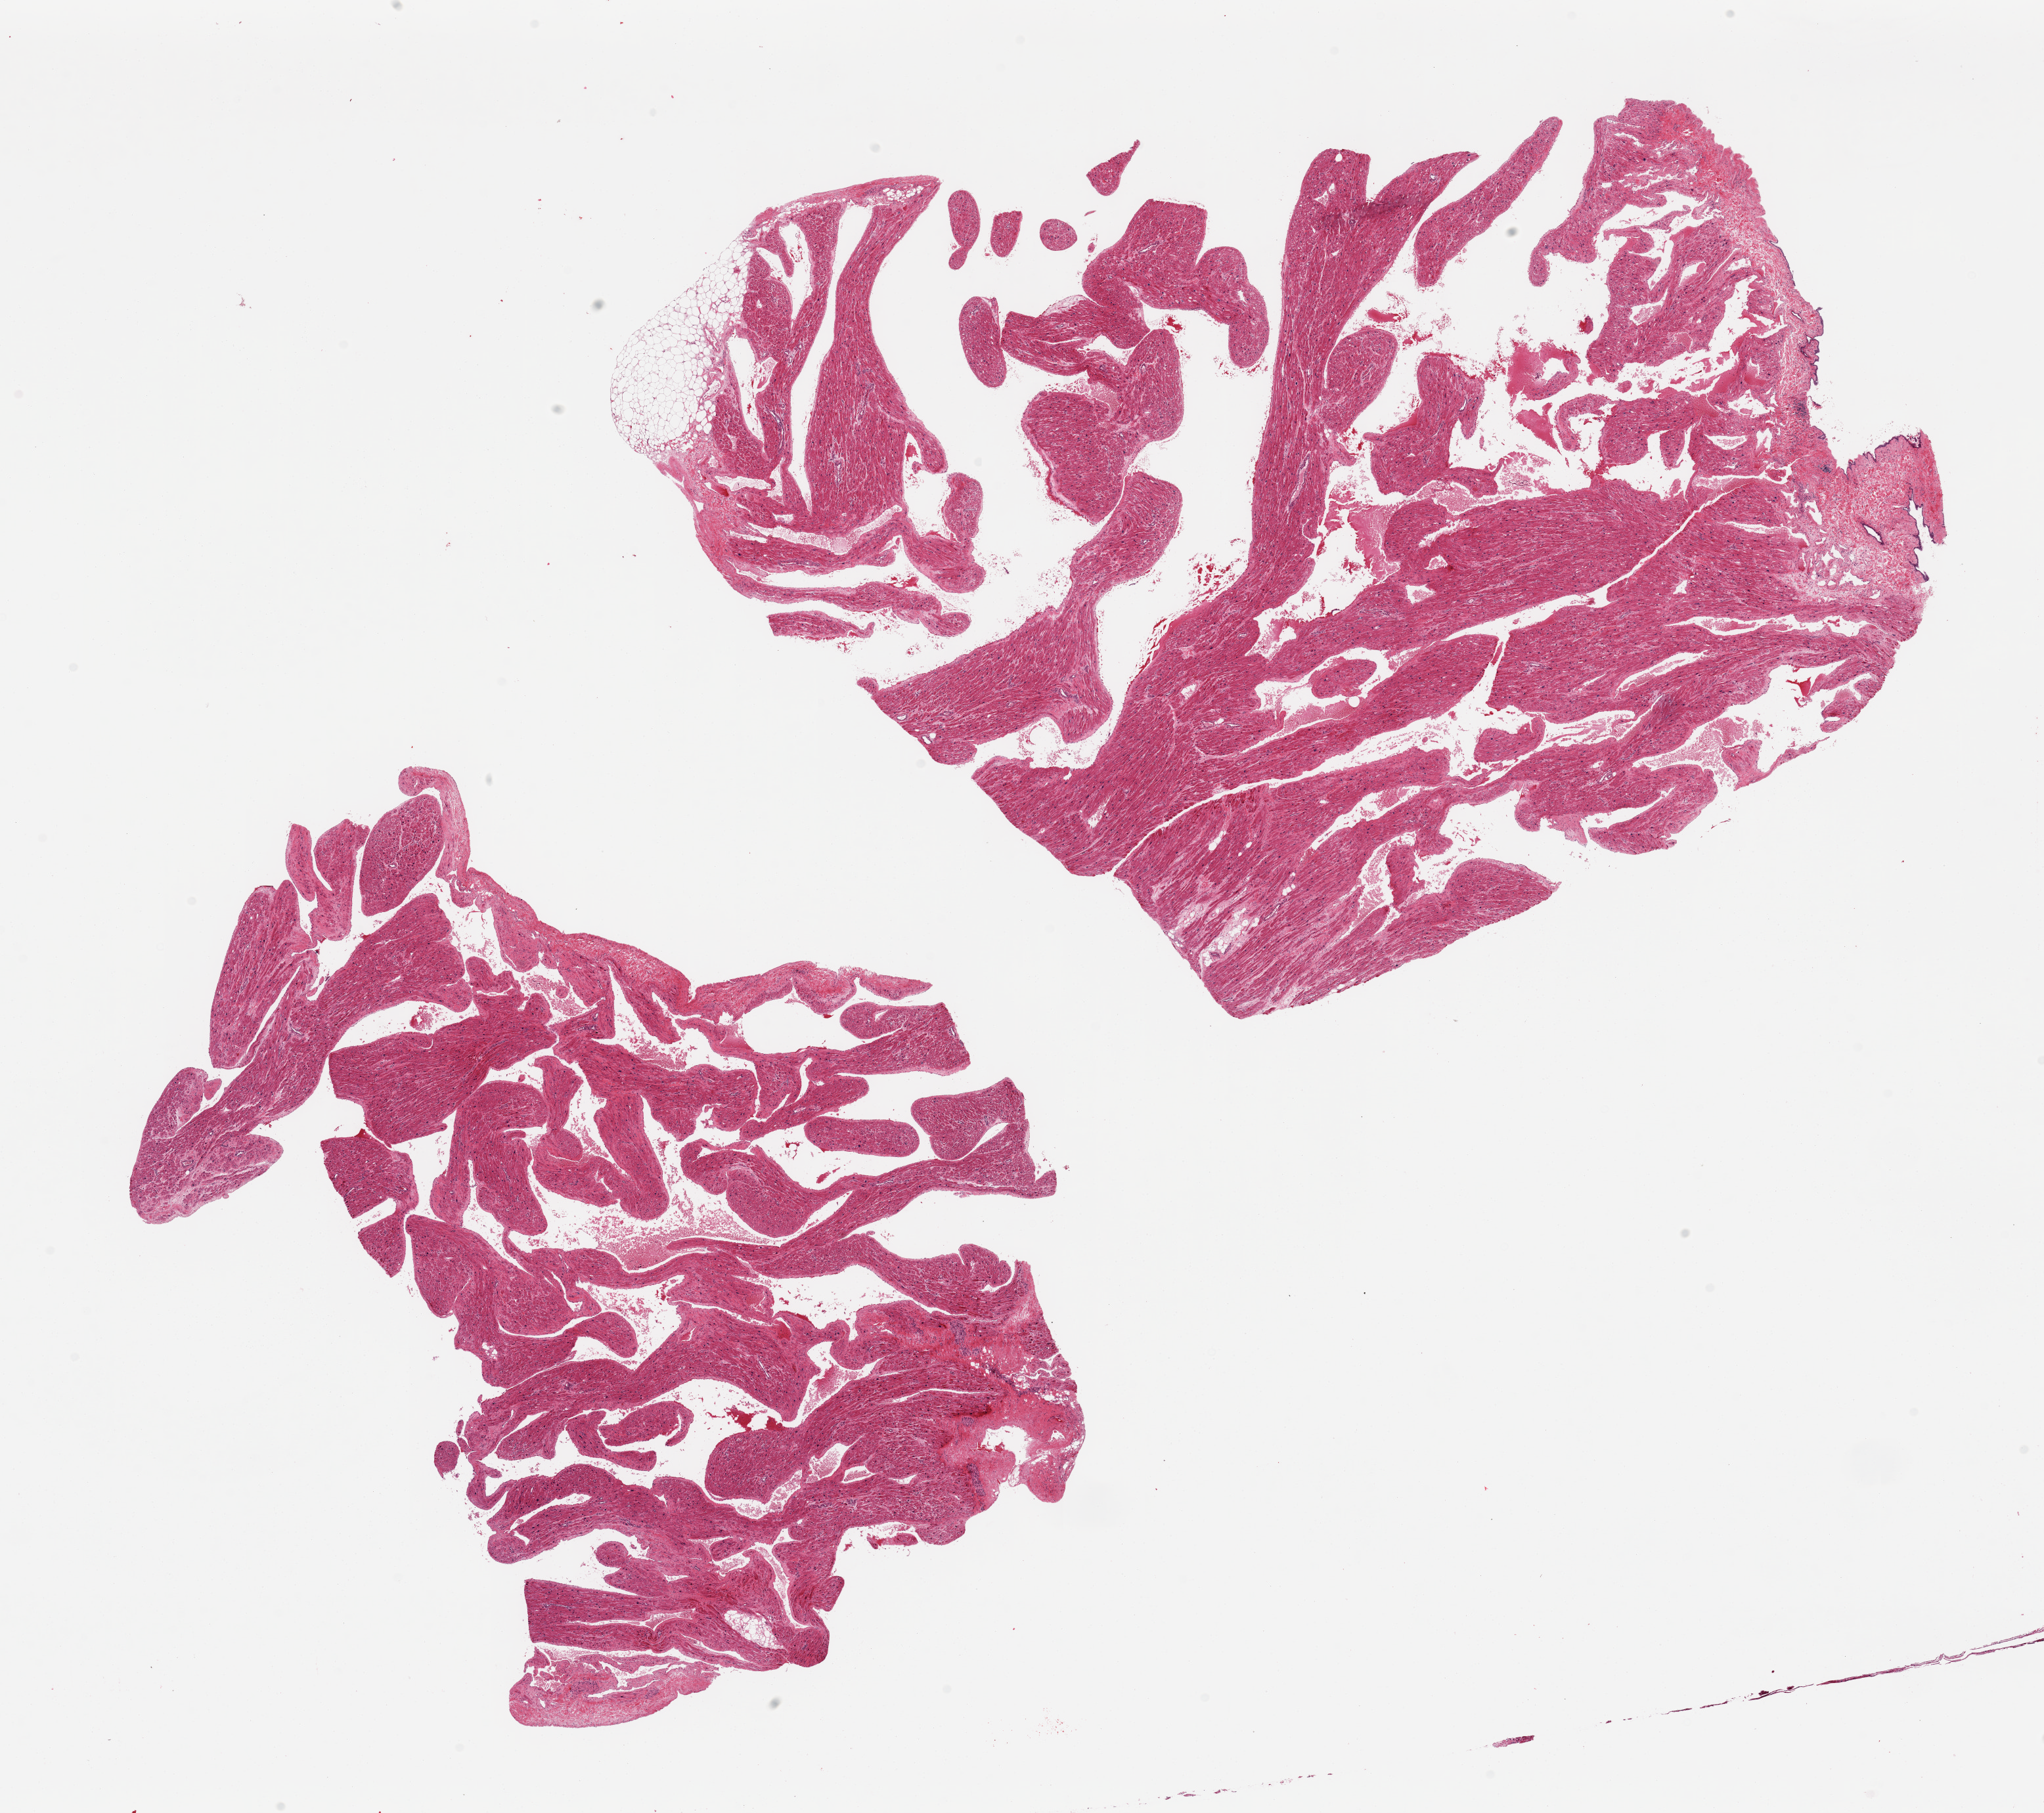
Whole-slide image, hematoxylin and eosin (H&E) stain — a low-resolution overview of the entire scanned area, about 24.6 x 21.8 mm, PAXgene-fixed, paraffin-embedded tissue, target tissue: auricular appendage, donor tissue sample. Donor: male.
• review note (as recorded): 2 pieces, no abnormalities